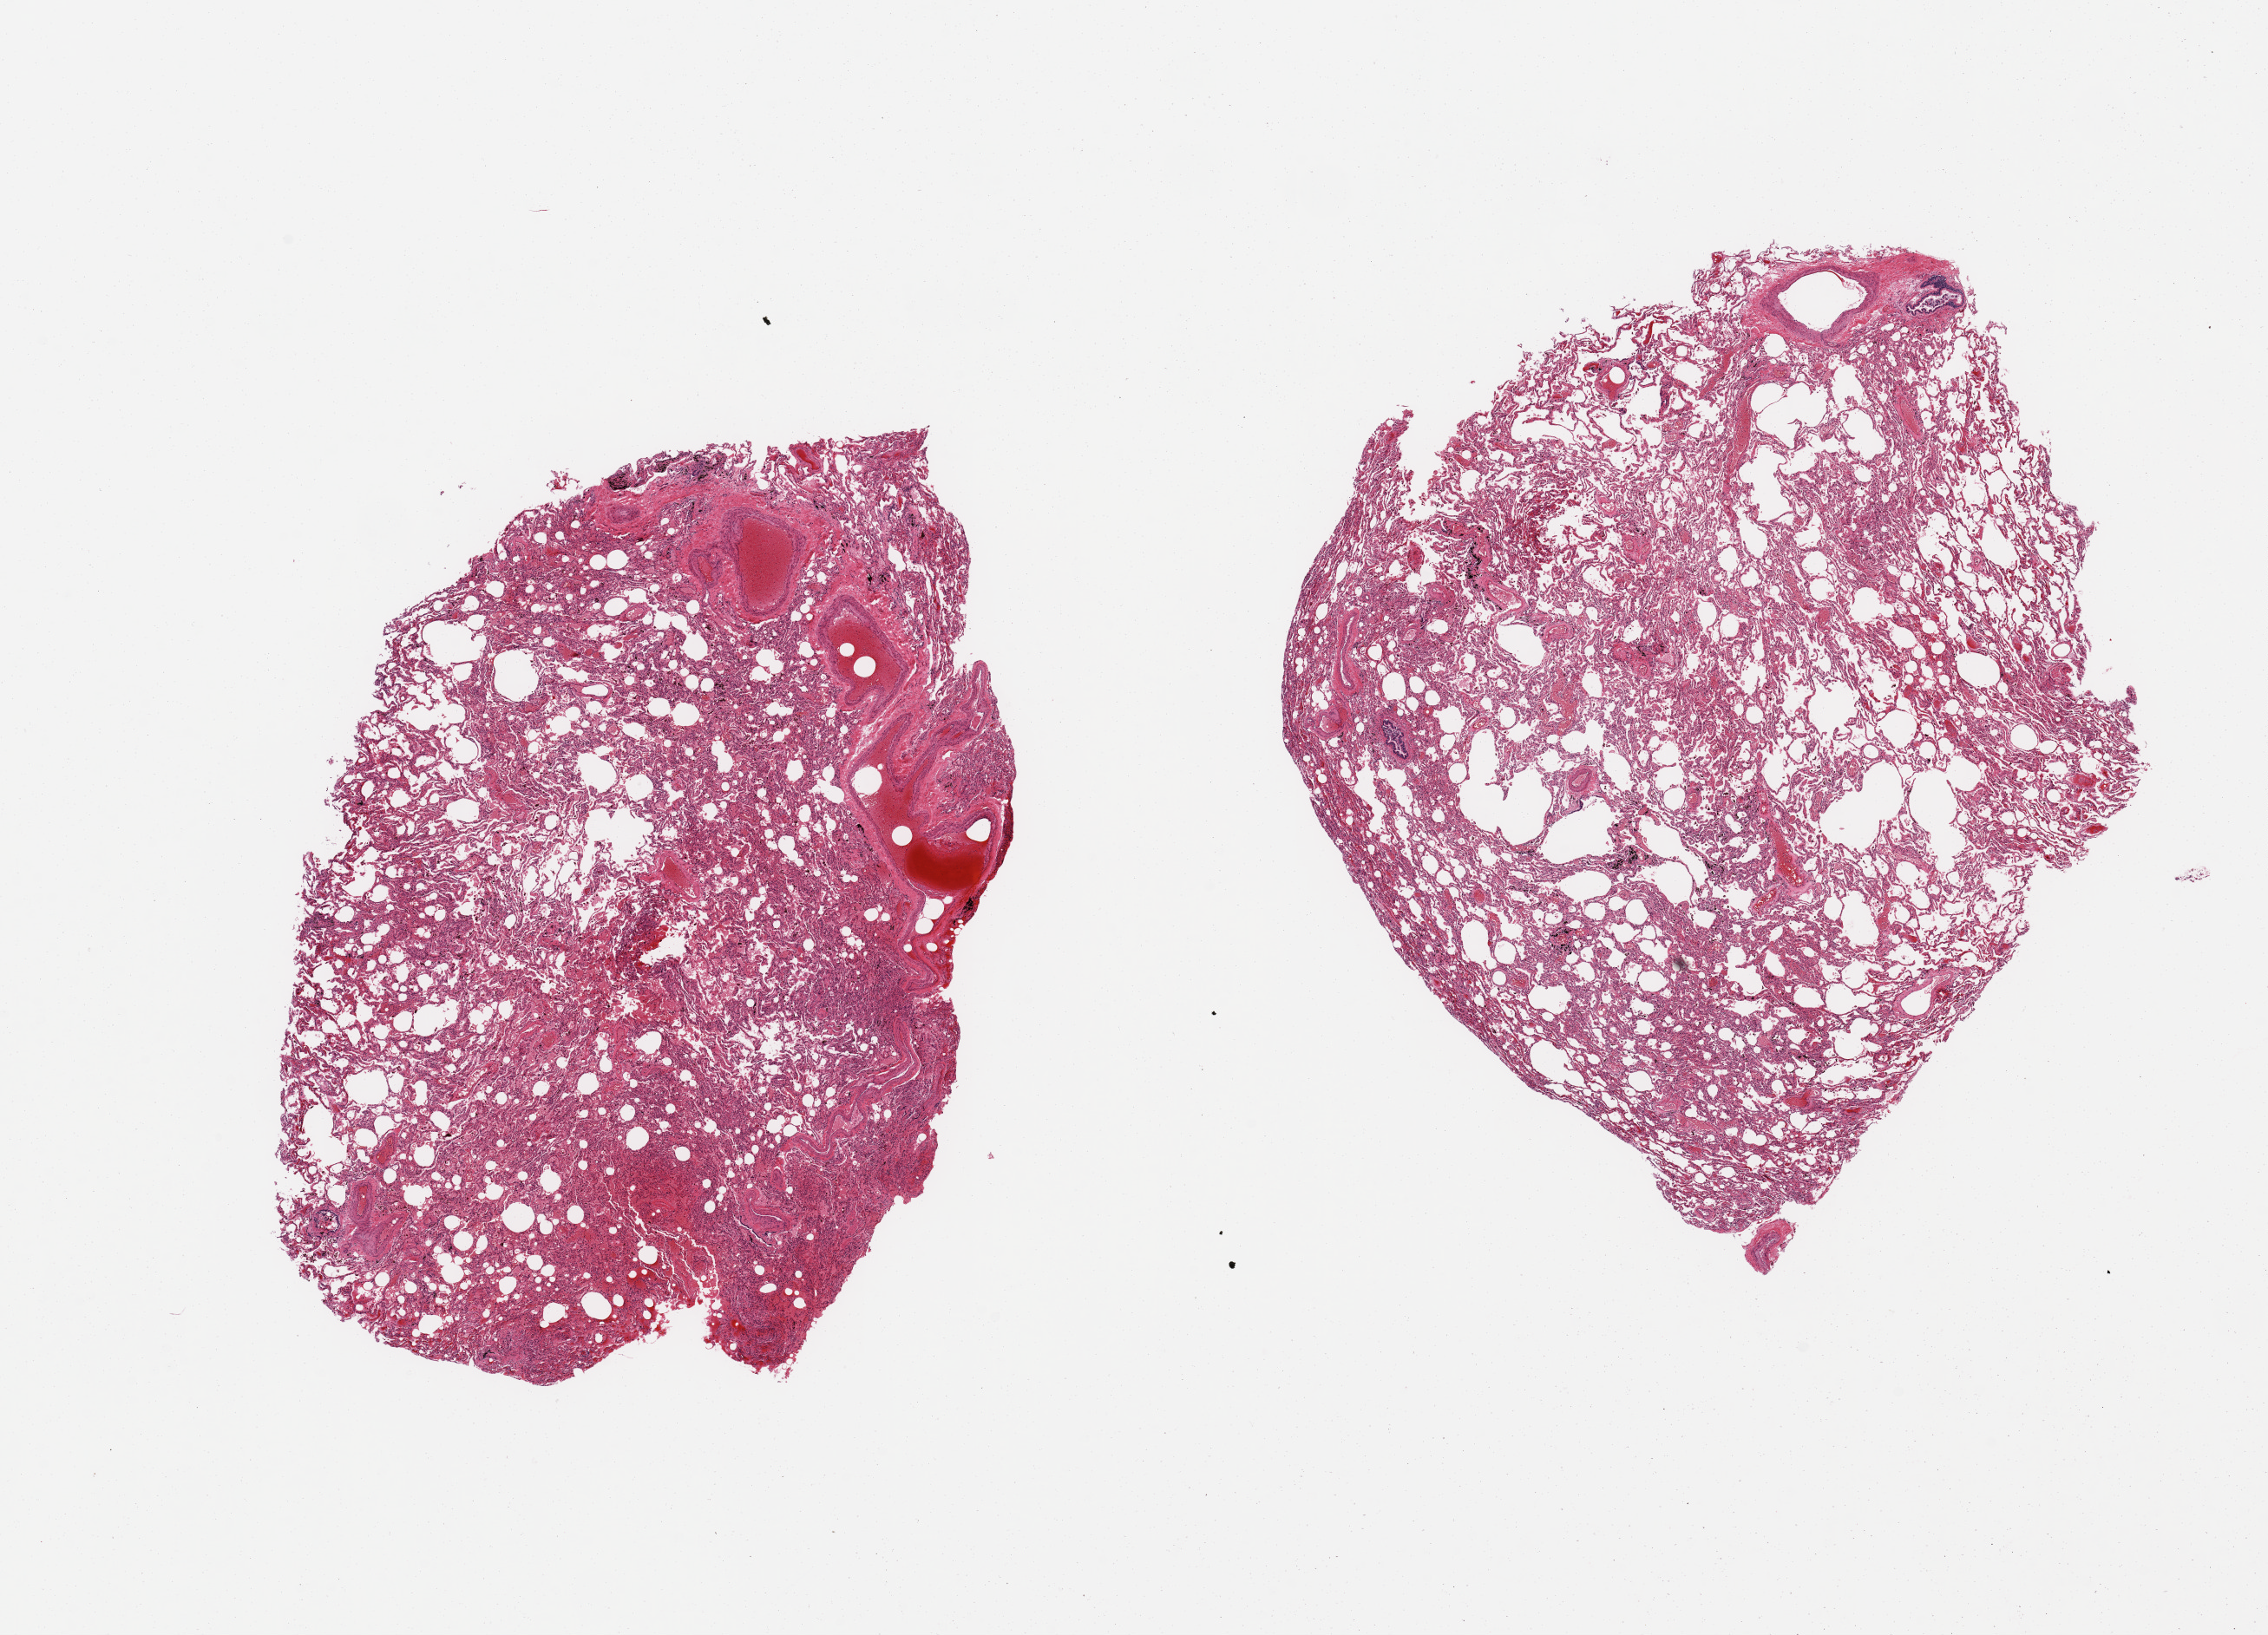
Whole-slide image, hematoxylin and eosin (H&E) stain — a low-resolution overview of the entire scanned area, about 20.7 x 14.9 mm. PAXgene-fixed, paraffin-embedded tissue. Section of lung (target tissue). Donor tissue sample. Male donor.
Pathologist's review note for this sample: 2 pieces; foci of emphysema; several engorged large blood vessels in 1 piece [10%]; patchy alveolar hemorrhage.